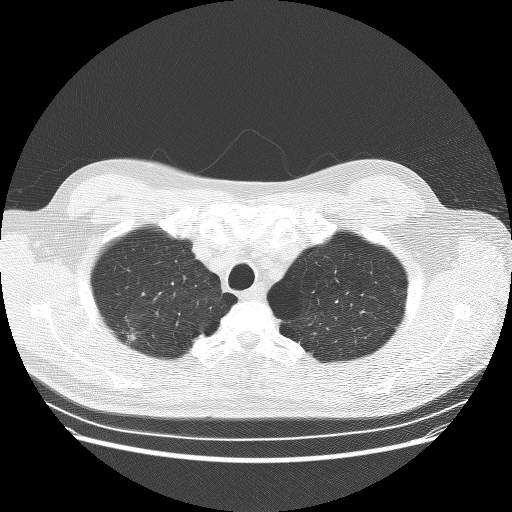
Low-dose screening chest CT, one axial slice. Slice 226 of 253 in the series (ordered by position). Reconstruction kernel BONE. 120 kVp. Lung window (W 1500 / L -600 HU). 512 × 512 image matrix, field of view 370 × 370 mm.
Outlined on this slice (manually delineated by an expert):
- lesion 1 (tumor, upper lobe of right lung): bounding box [x1, y1, x2, y2] px = [129, 334, 135, 340]